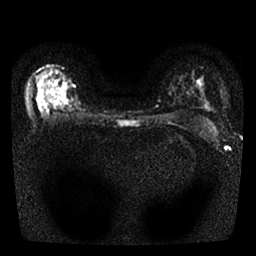
Breast MRI, one axial slice. Position 20 of 25 along the scan axis. Diffusion-weighted series; image 2 of 4 stored at this slice position (different b-values; order by instance number). 1.5 T. 4 mm slice thickness. 256 × 256 image matrix, field of view 300 × 300 mm. Female patient.
Outlined on this slice (manually delineated by an expert):
- tumour on diffusion-weighted imaging: bounding box [x1, y1, x2, y2] px = [38, 92, 43, 104]